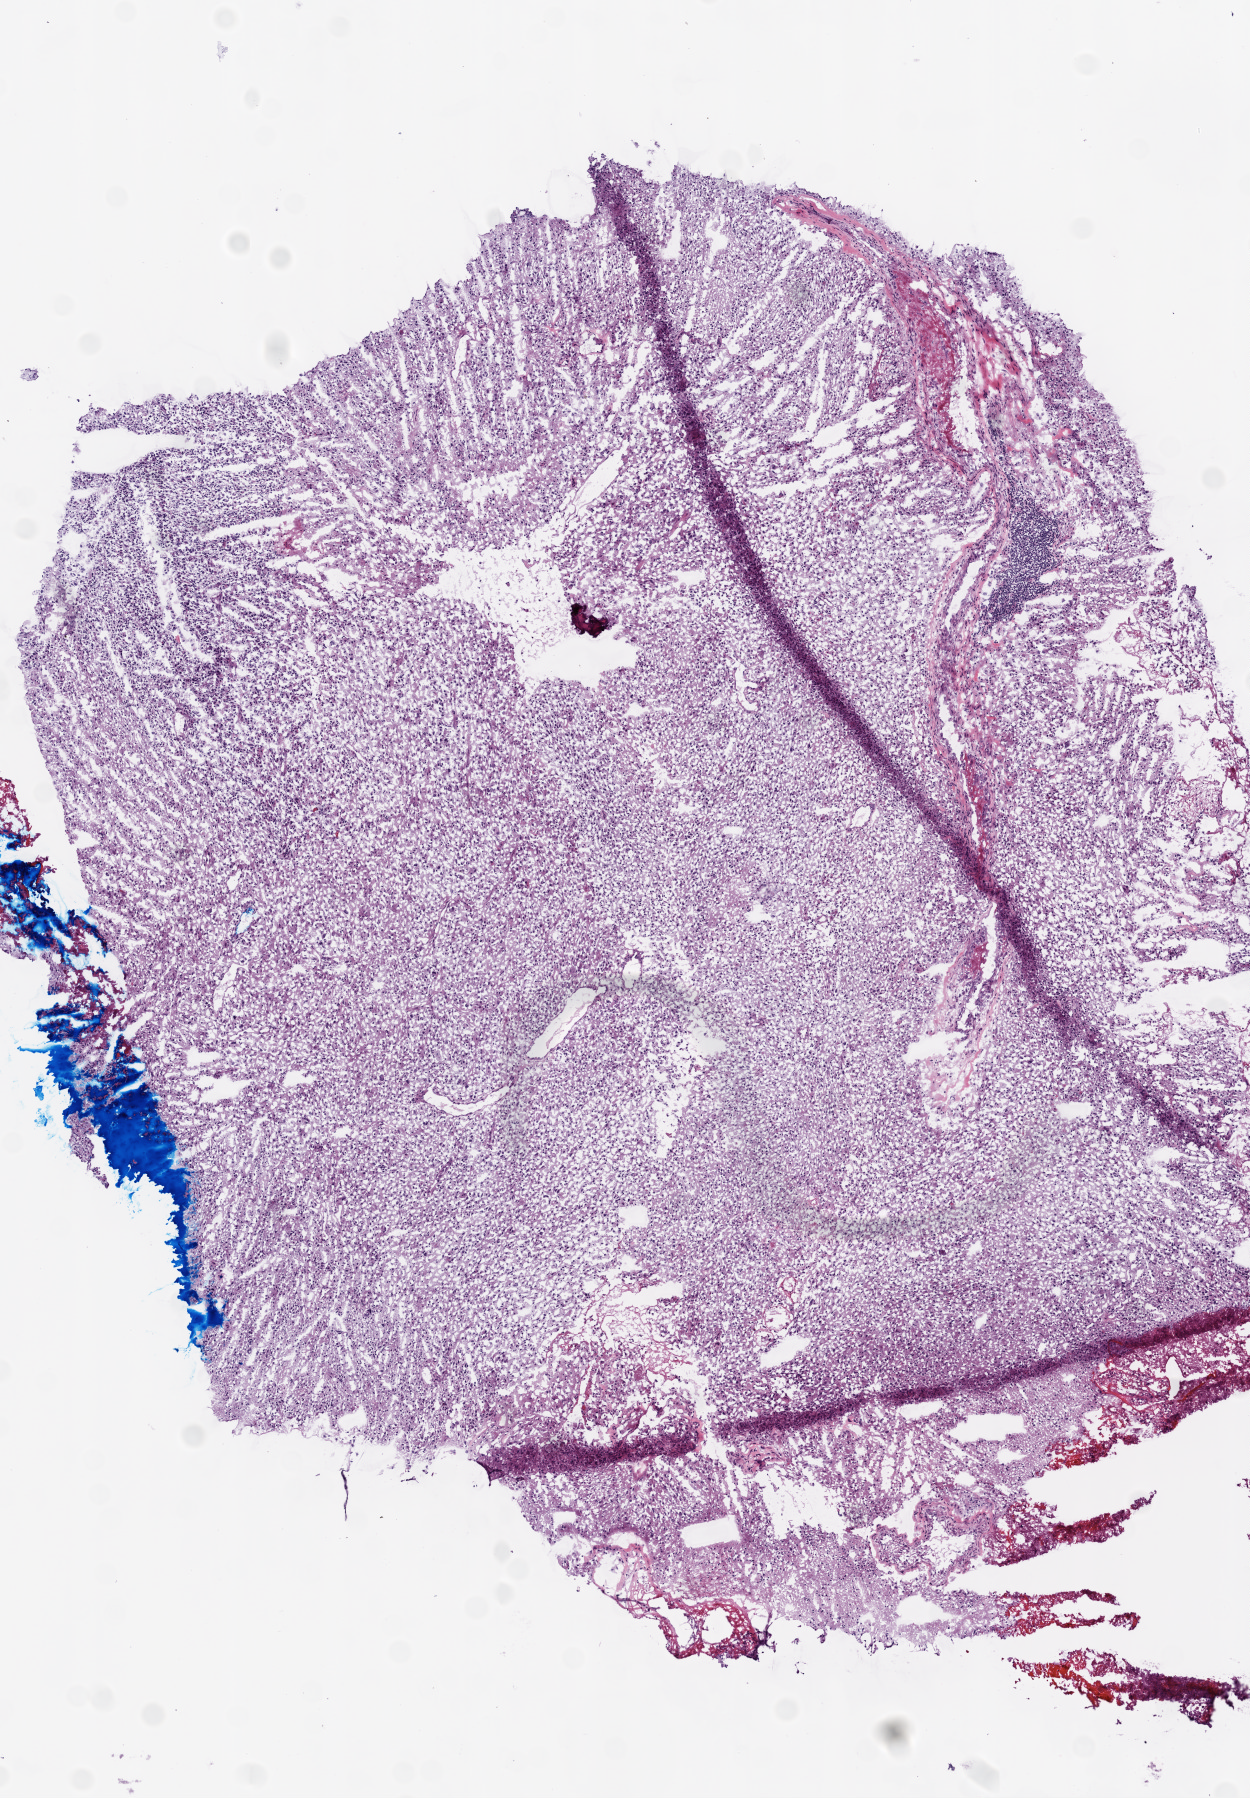
Whole-slide histology image, H&E, shown as a low-resolution overview of the whole scanned area (about 5.0 x 7.2 mm, acquisition: 20x scan). Frozen section from the bottom of the tissue portion. Brain, primary tumour sample. Male patient; age at initial diagnosis 65 years. Pathologist review of this section (percent, as recorded): tumour cells 97%, tumour nuclei 80%, normal cells 0%, stromal cells 0%, necrosis 3%.
Histologic diagnosis: Glioblastoma.